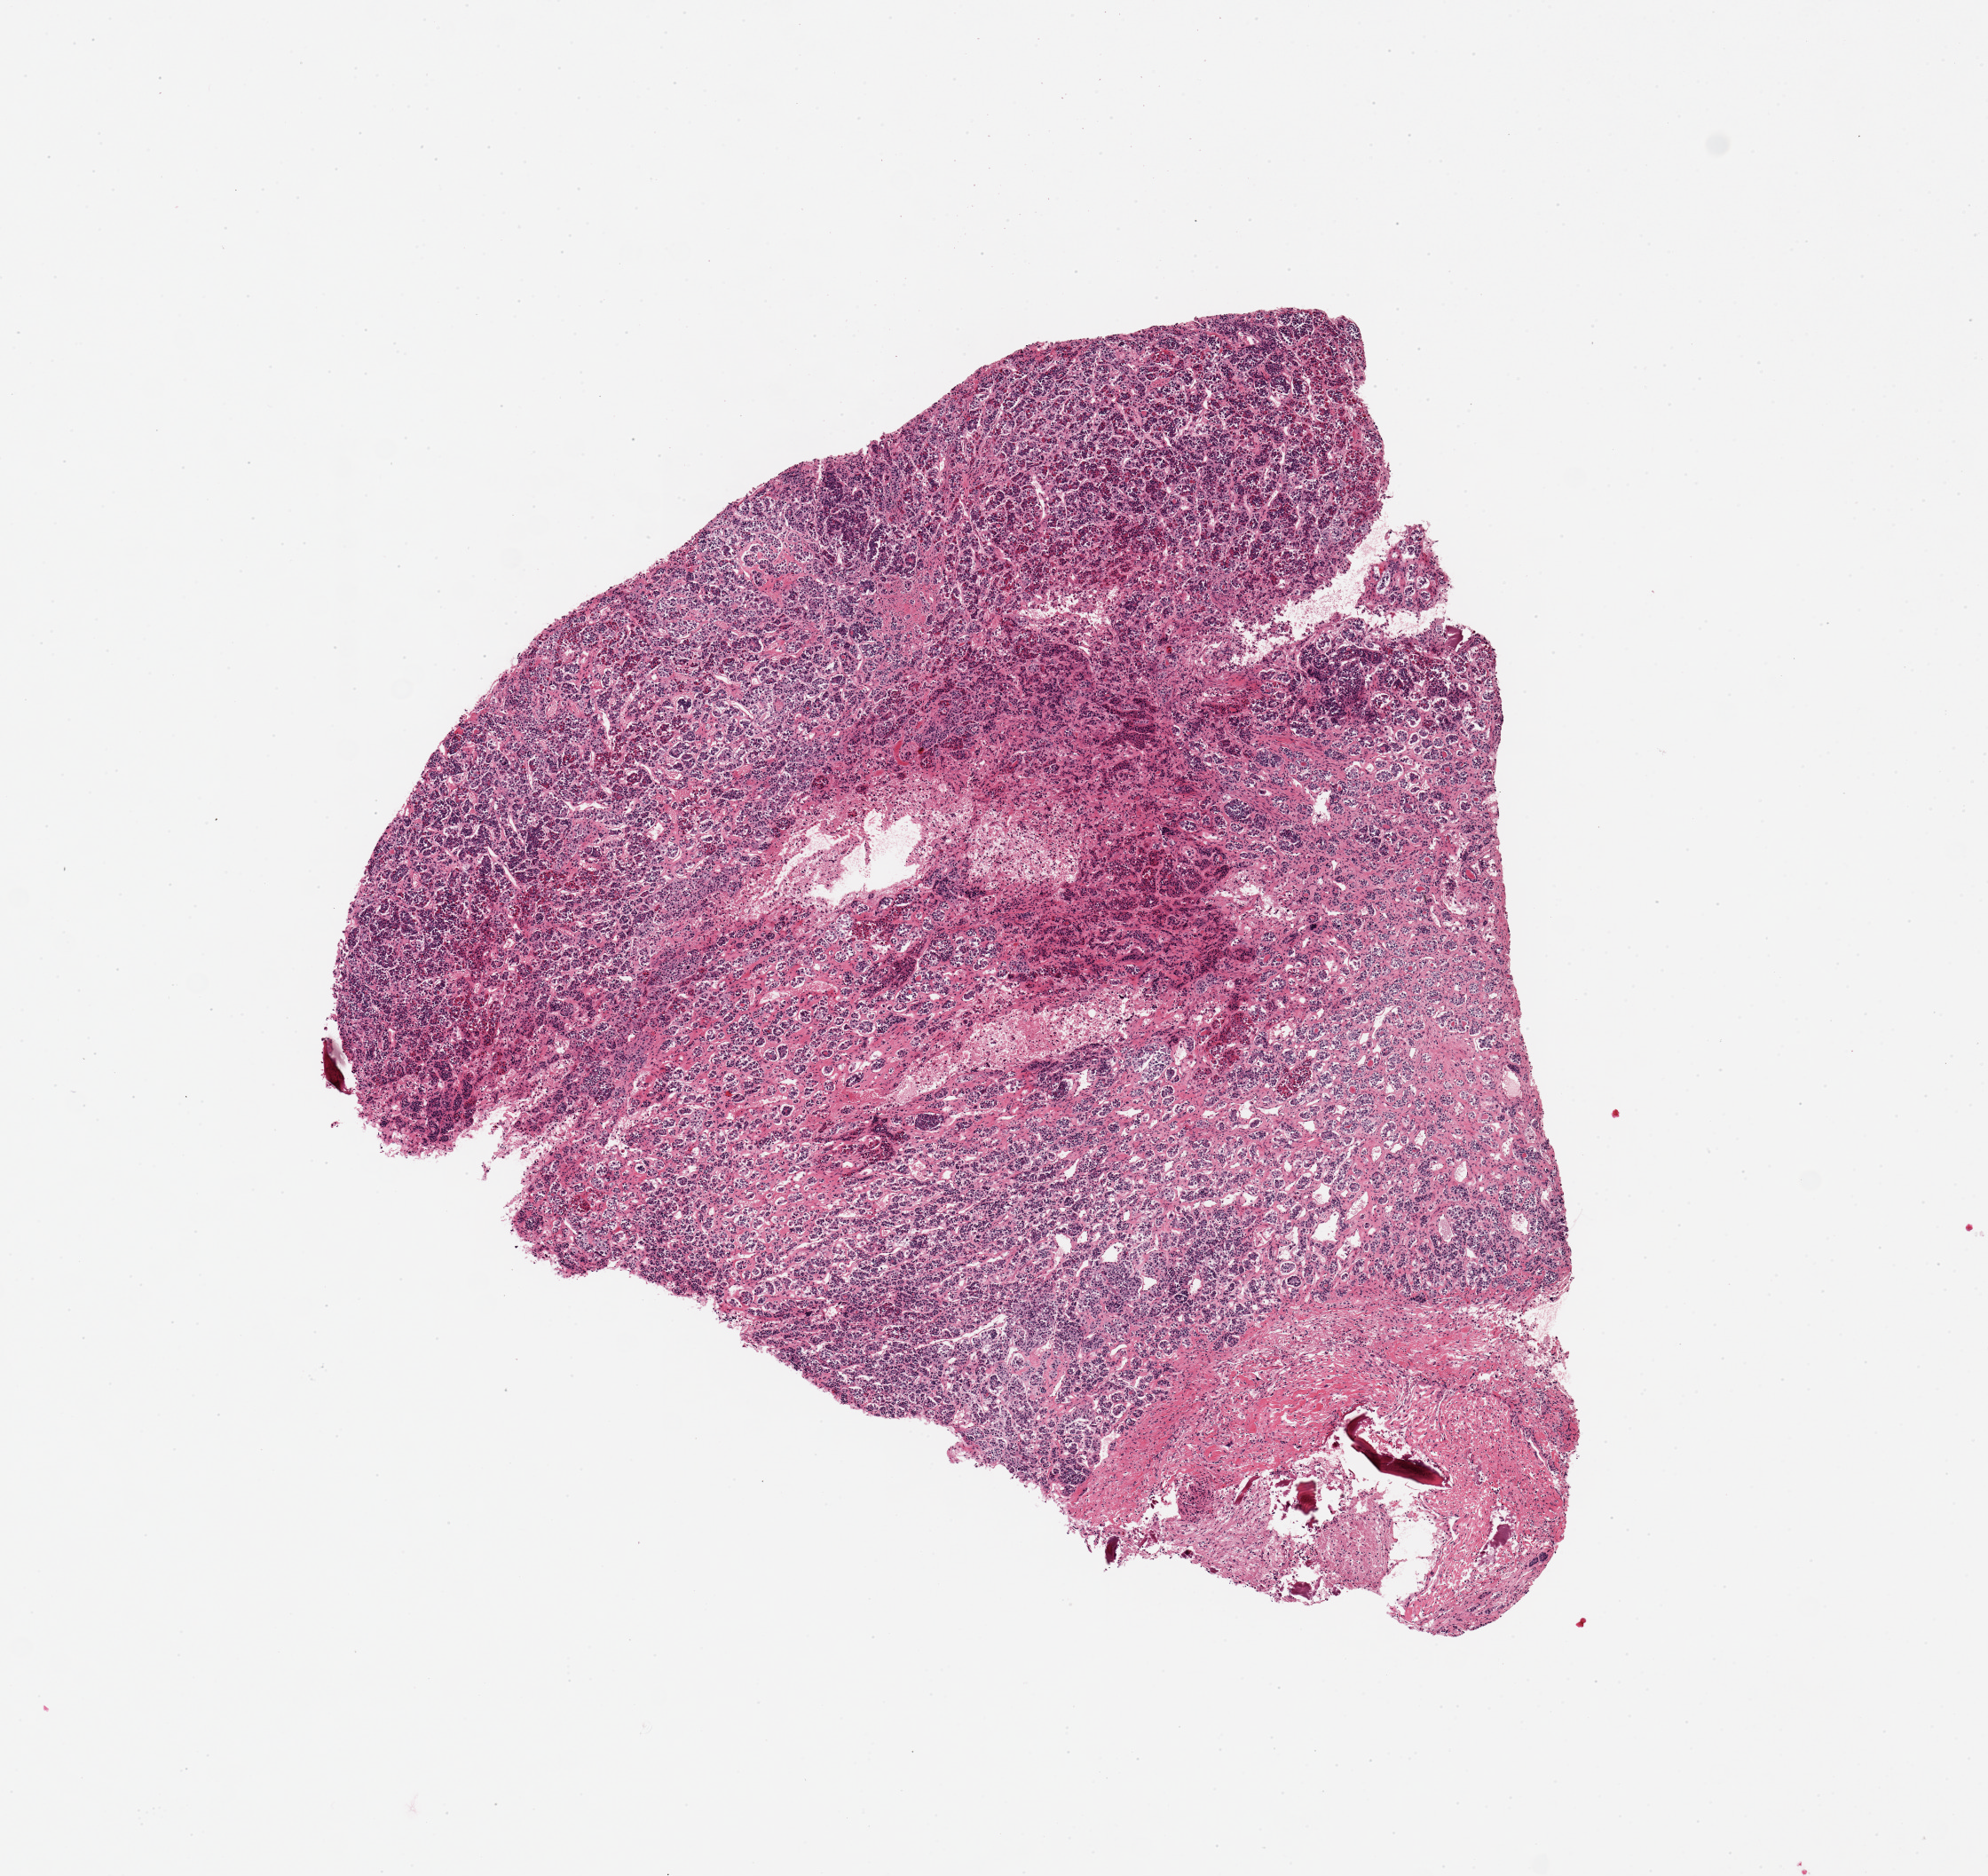
Whole-slide image, haematoxylin and eosin stain — whole scanned area (about 8.9 x 8.4 mm, acquisition: 20x scan) shown as a low-resolution overview. PAXgene-fixed, paraffin-embedded tissue. Section of pituitary (target tissue). Donor tissue sample. Donor: female.
Pathologist's review note for this sample: 1 pieces; ~10% of specimen is neurohypophysis; rest is adenohypophysis.